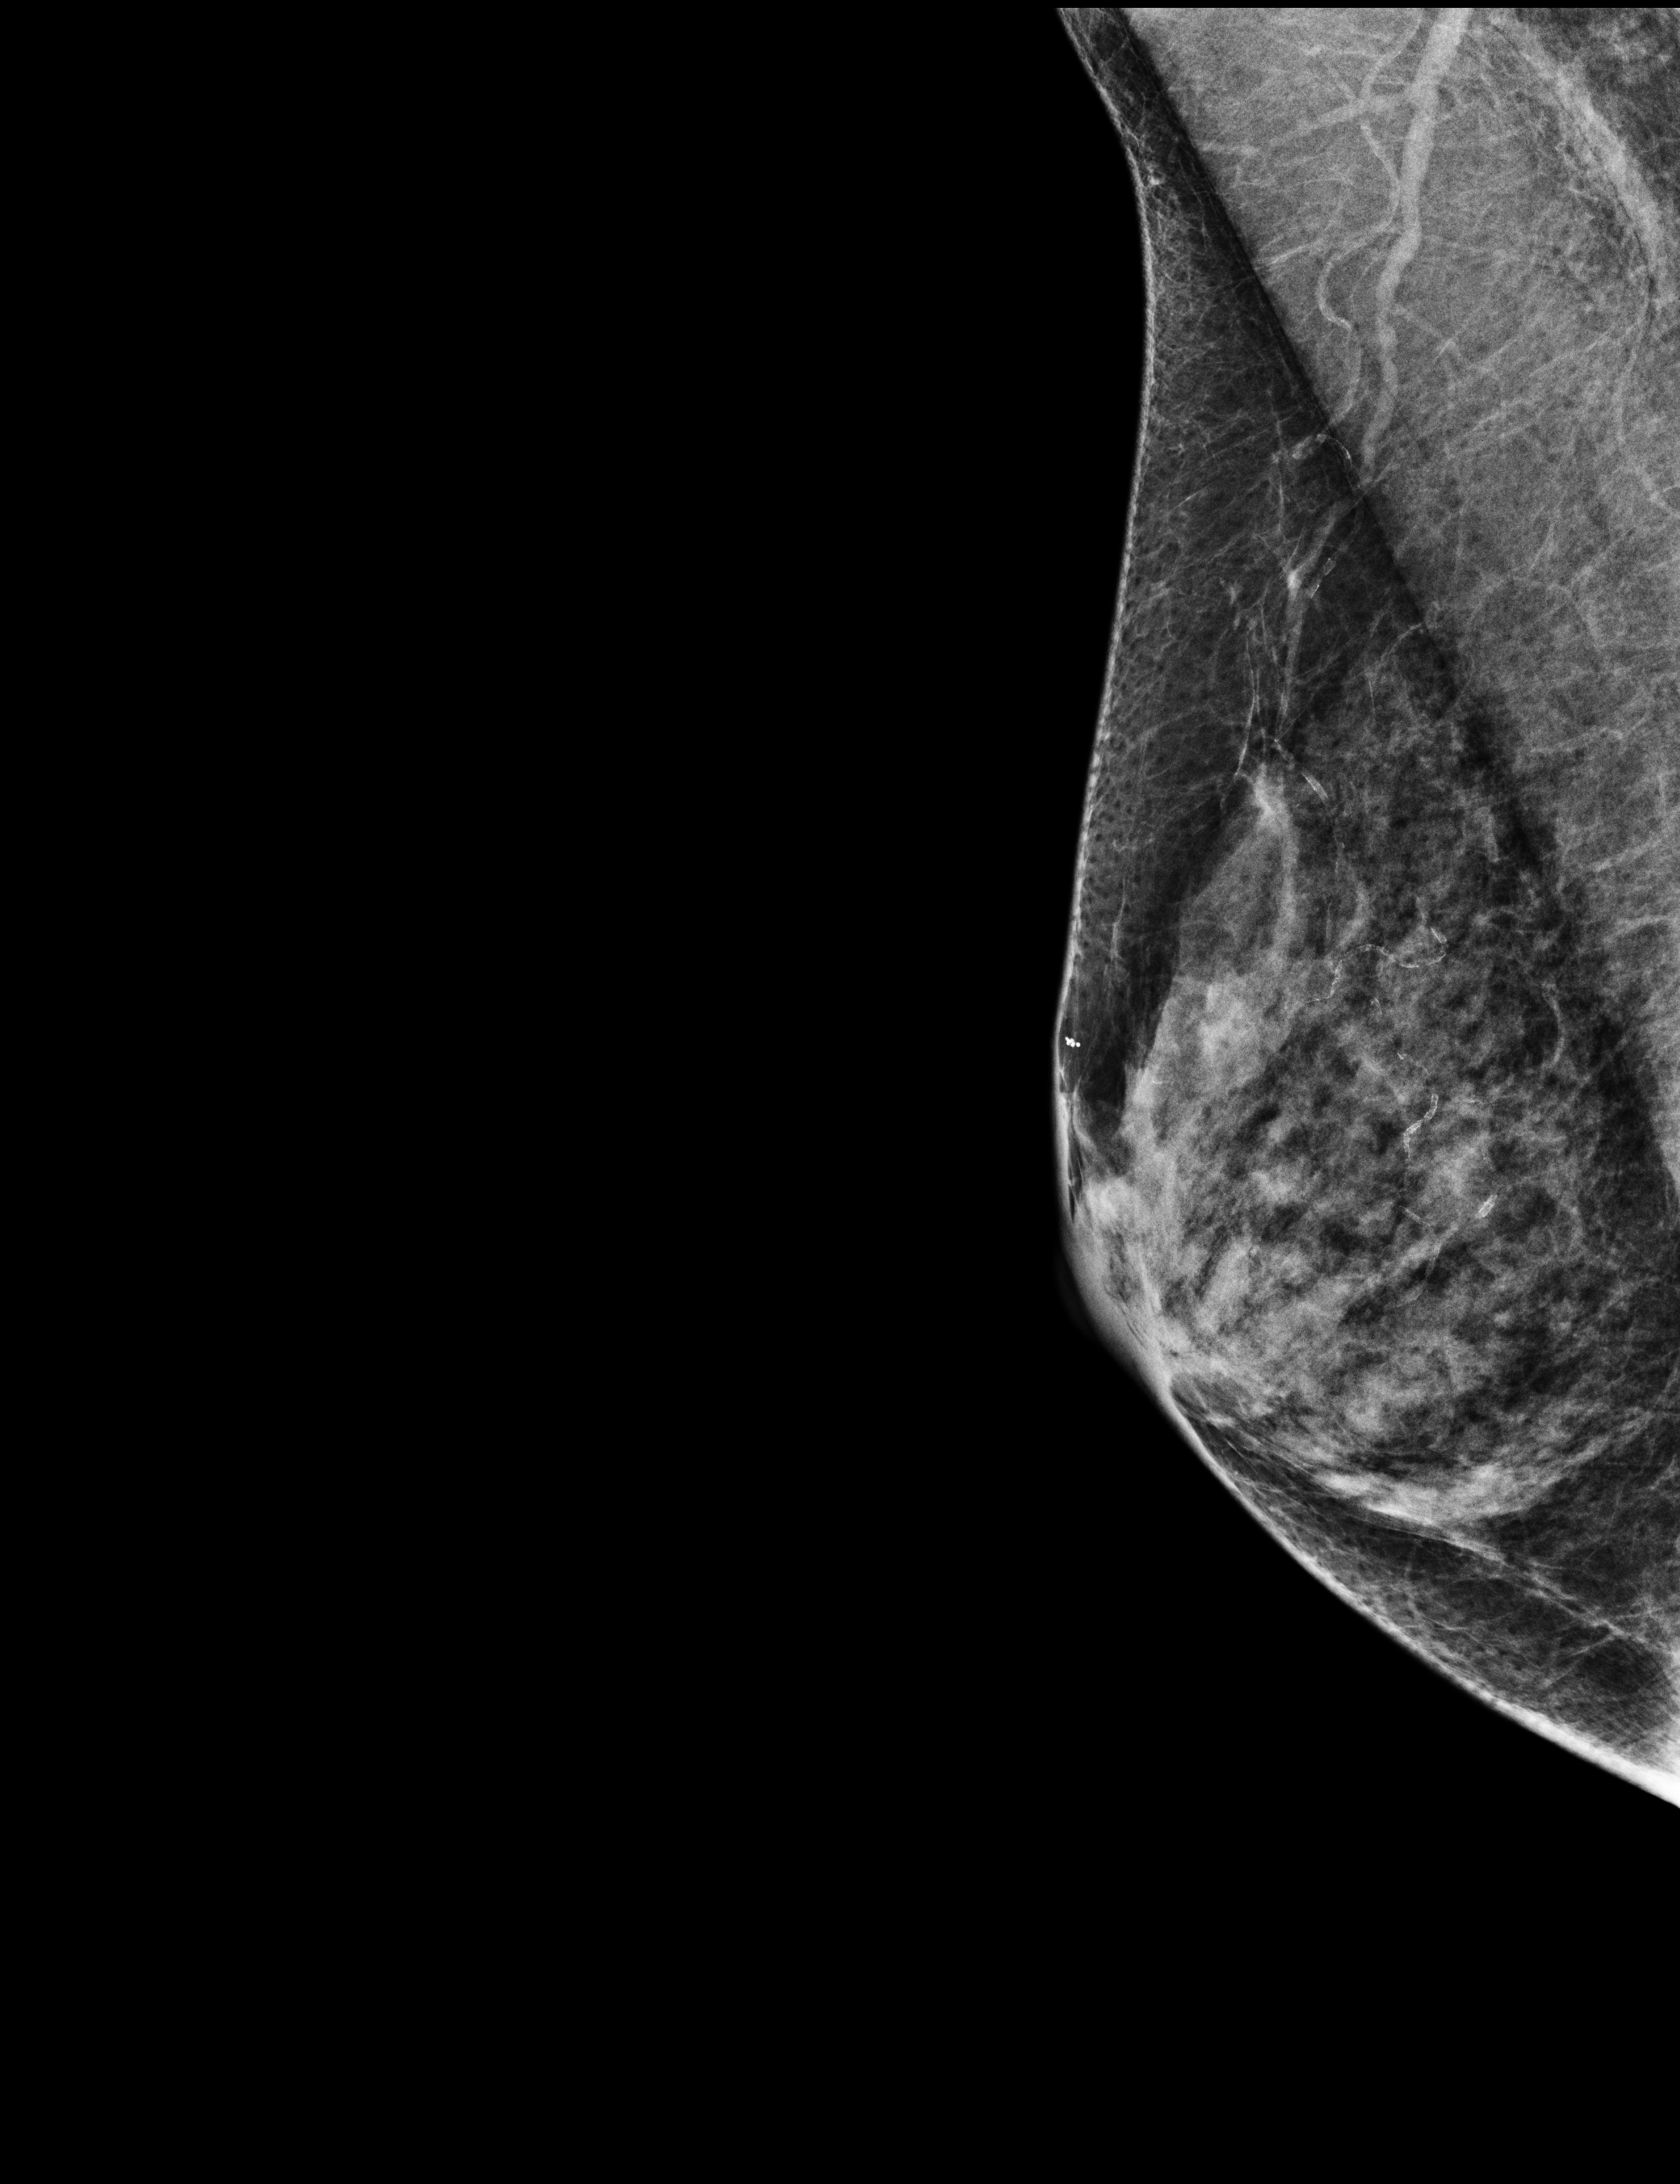
Annual screening mammography examination; compressed breast thickness 37 mm; system: Selenia Dimensions. Female patient, age 65 years.
Image type: full-field digital mammogram. Breast: right. Projection: MLO view.